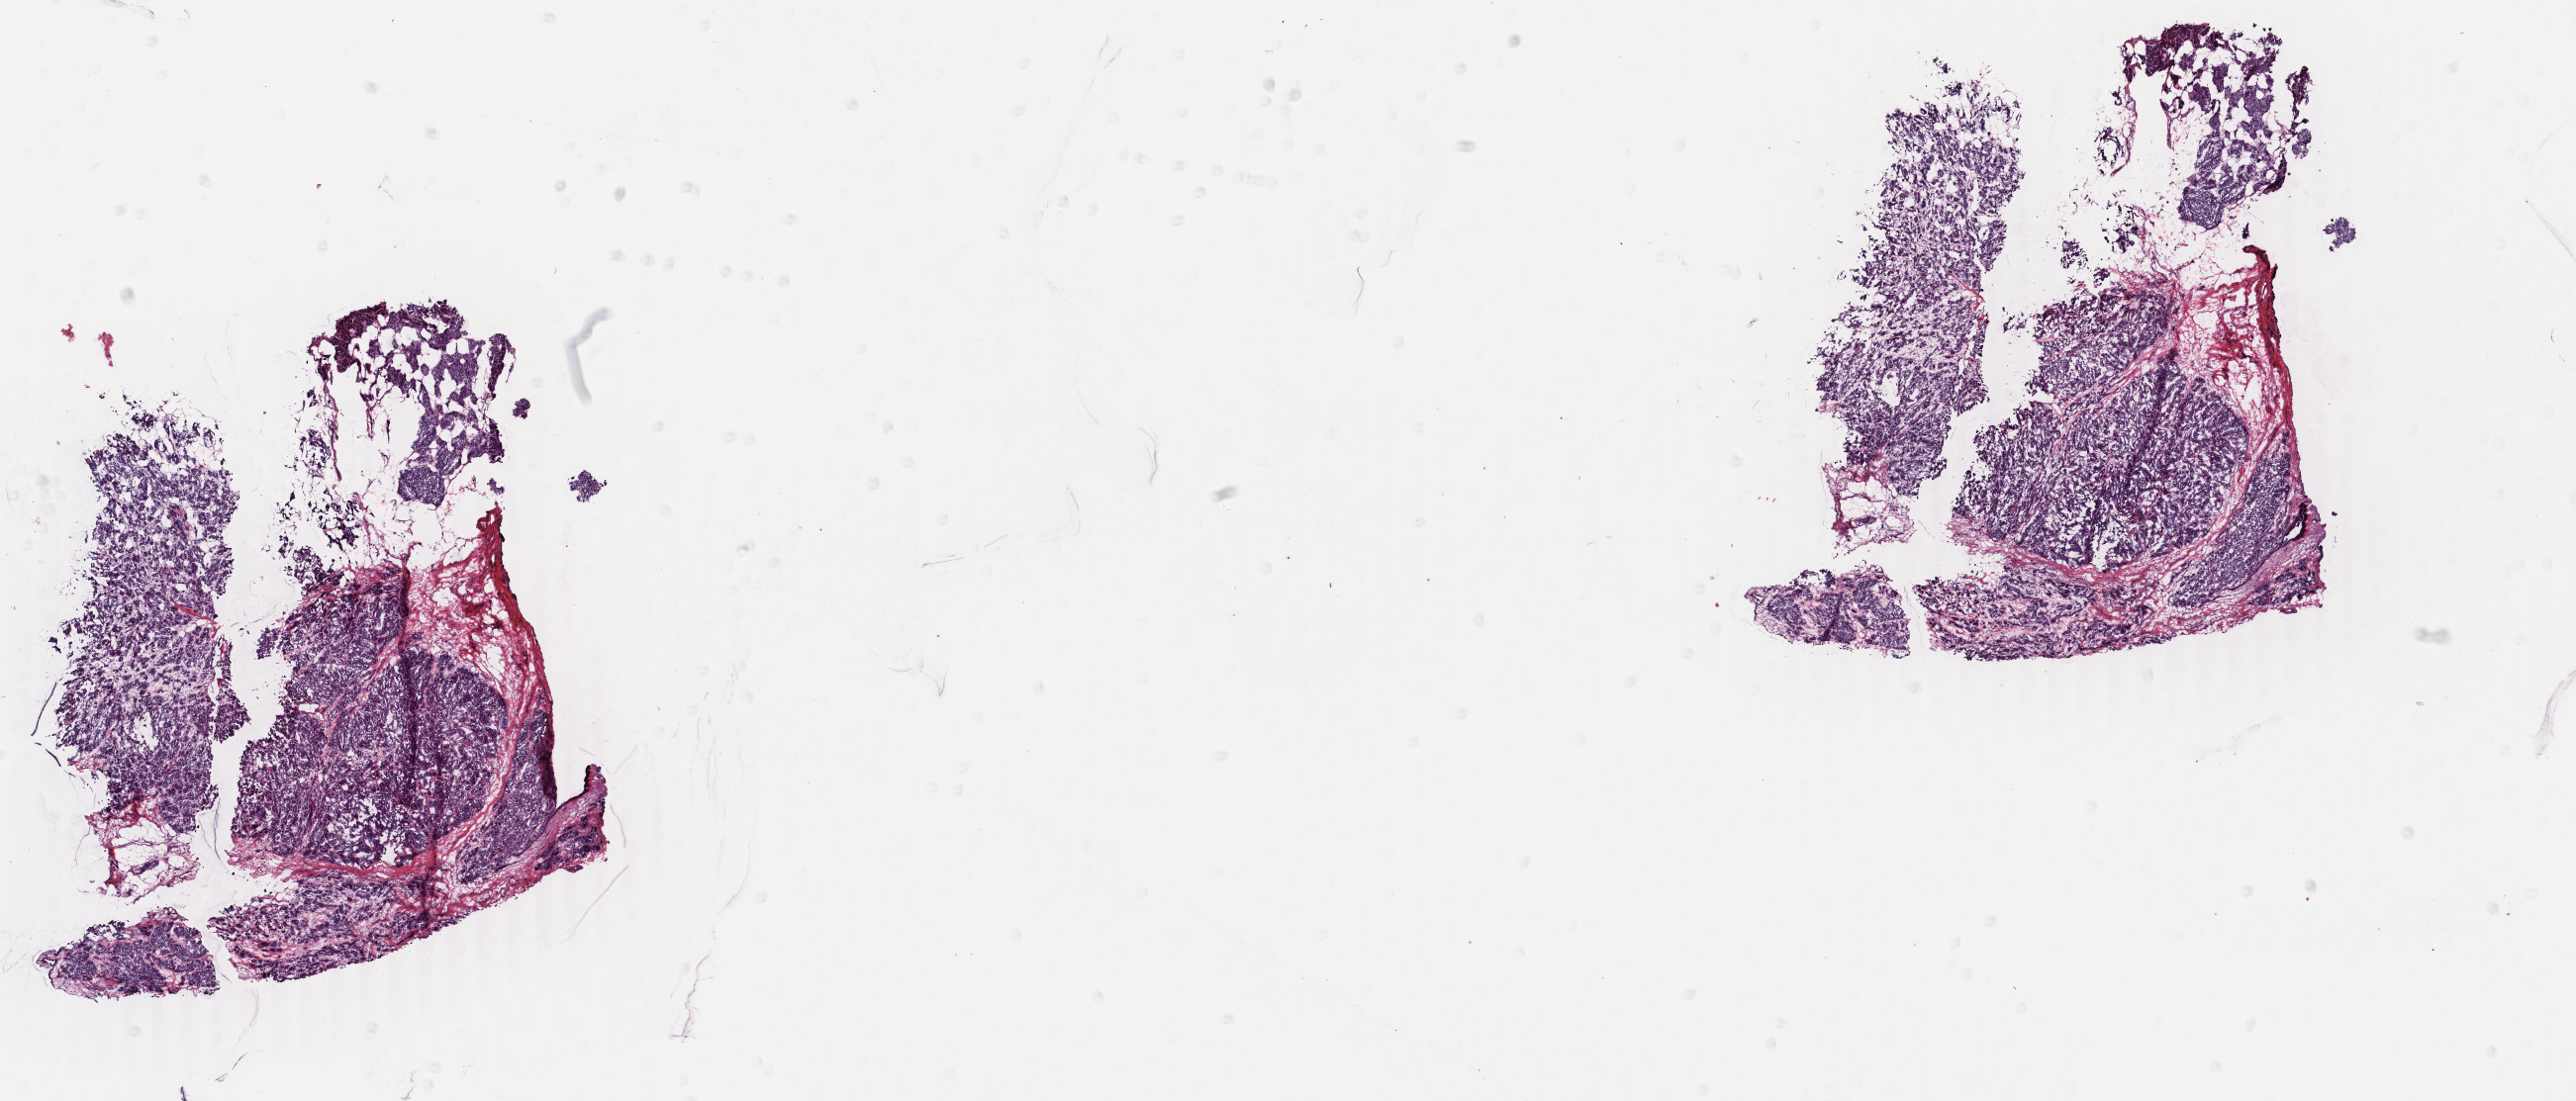
Digitized Hematoxylin and eosin (H&E) stained tissue section (whole slide) — a low-resolution overview of the entire scanned area, about 20.7 x 8.9 mm. Frozen section from the bottom of the tissue portion. Breast, primary tumour sample. Female, age 37 years at initial diagnosis. Pathologist review of this section (percent, as recorded): tumour cells 85%, tumour nuclei 85%, normal cells 0%, stromal cells 14%, necrosis 1%. Infiltration values recorded for this section: lymphocyte infiltration 1%, monocyte infiltration 0%, neutrophil infiltration 0%.
AJCC pathologic stage: IIB (6th edition). Histologic diagnosis: Infiltrating duct carcinoma, NOS. Lymph nodes positive (case pathology): 1 of 23 examined.